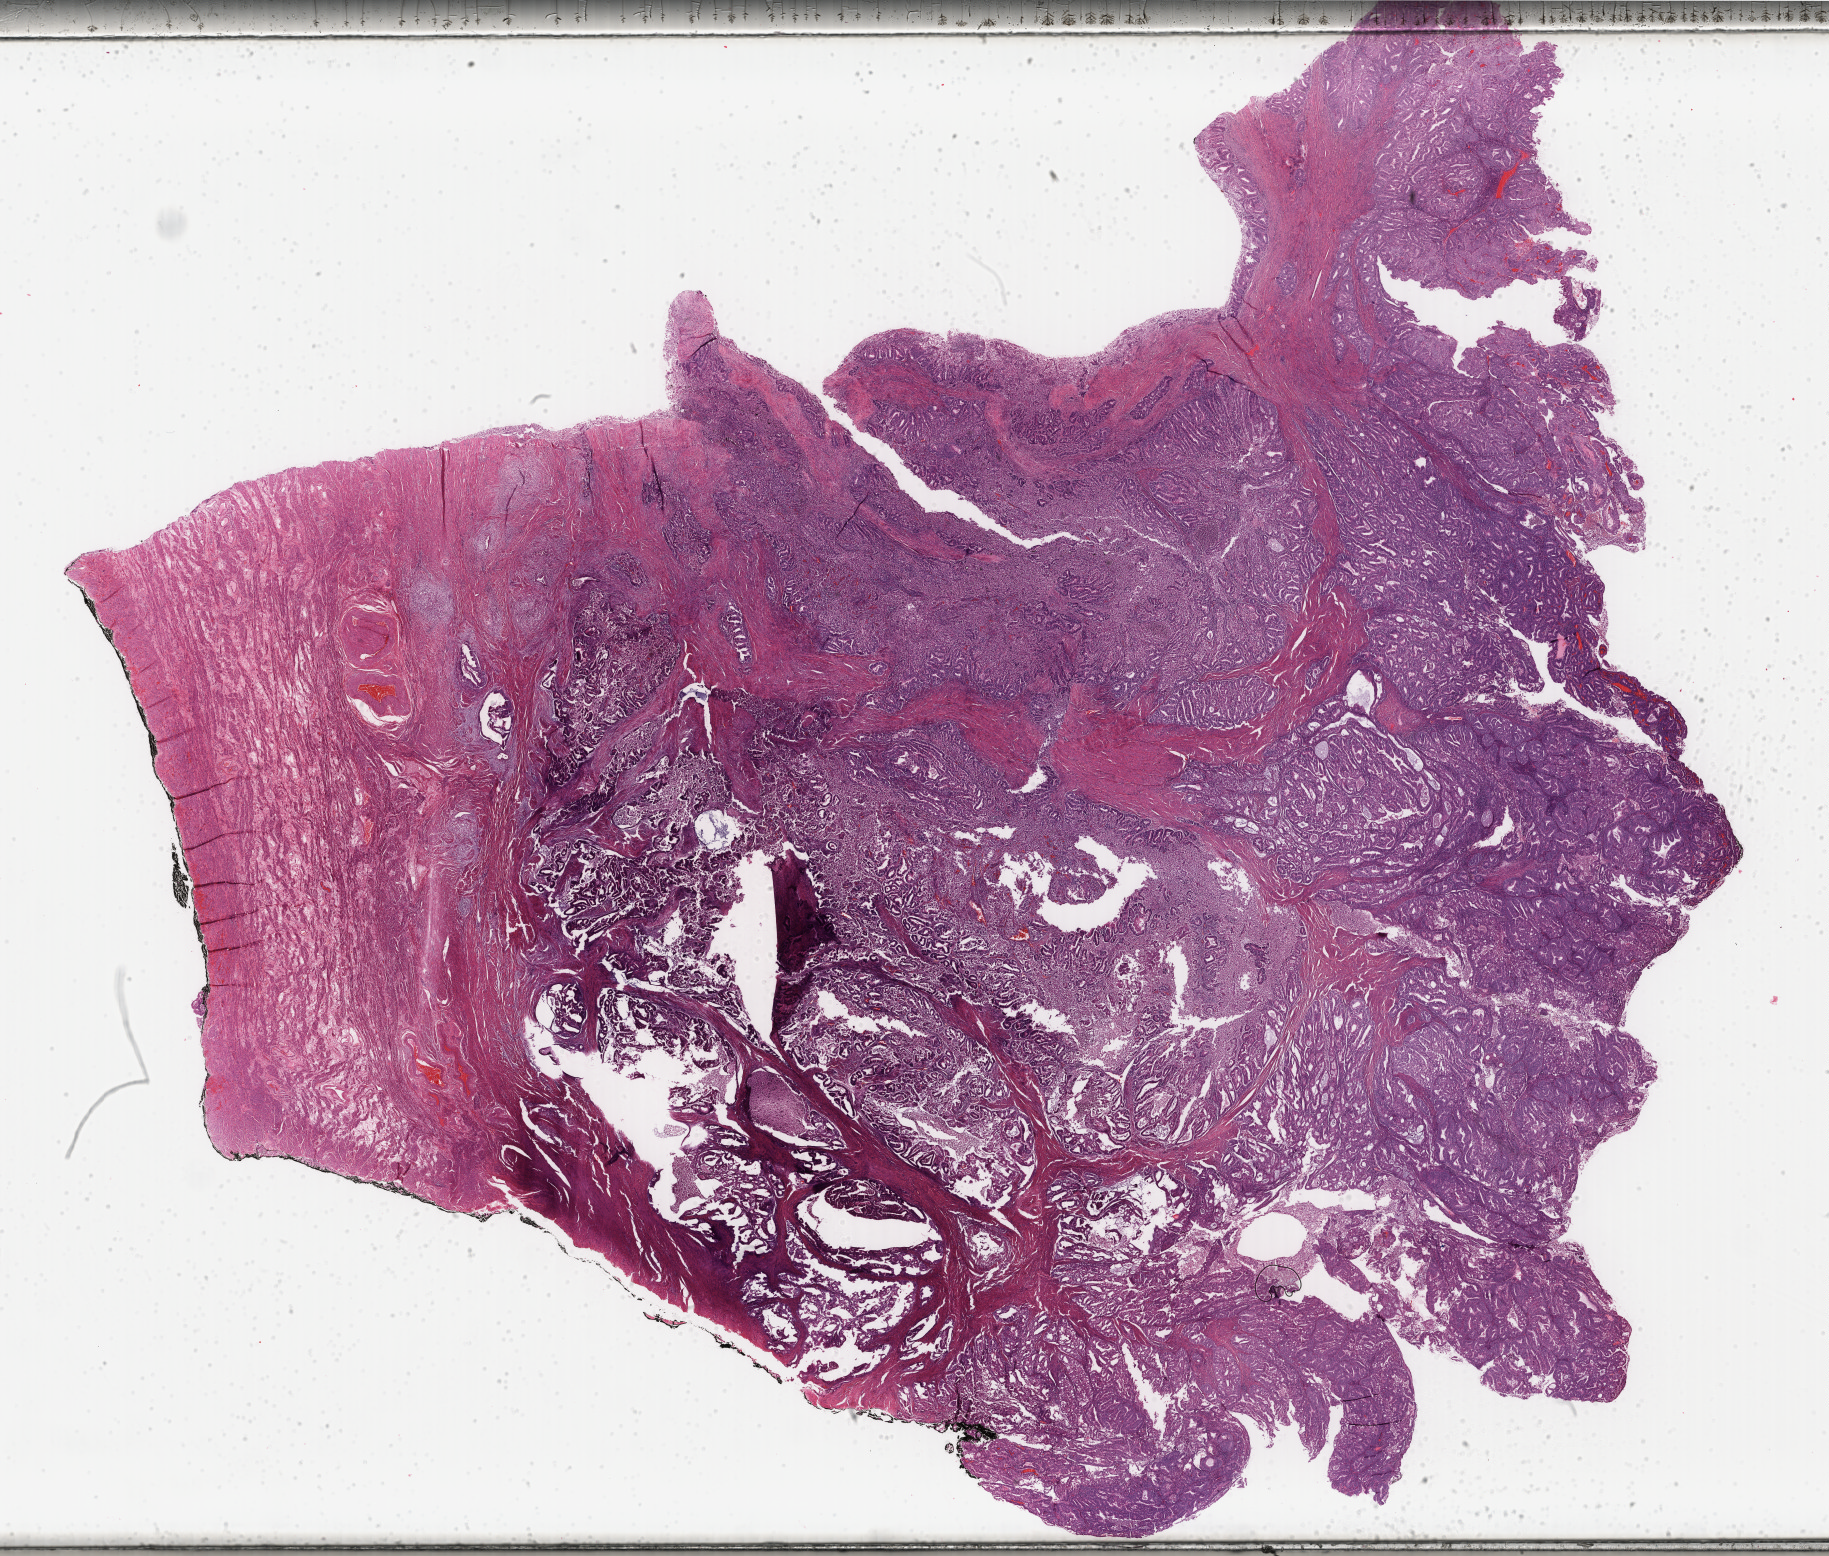
Whole-slide histology image, H&E-stained, whole scanned area (about 29.0 x 24.7 mm, from a 40x scan) shown as a low-resolution overview; formalin-fixed paraffin-embedded (FFPE) diagnostic section; uterus, primary tumour sample. Female patient; age at initial diagnosis 68 years. Histologic grade: G2 (moderately differentiated).
• FIGO stage: IB
• histologic diagnosis: Endometrioid adenocarcinoma, NOS (endometrium)
• lymph nodes positive (case pathology): 0 of 6 examined